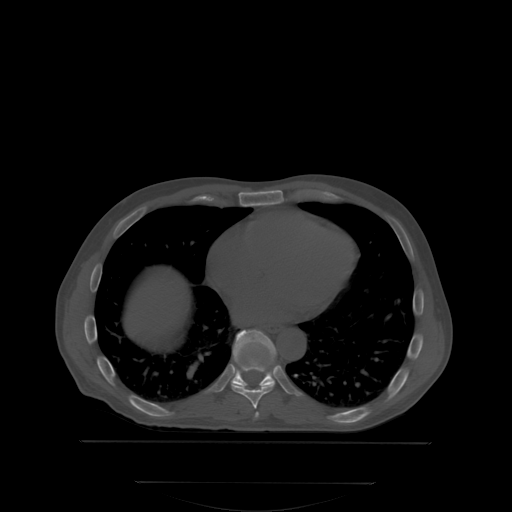
CT including the spine, one axial slice. Position 211 of 350 along the scan axis. Bone window (W 1800 / L 400 HU). 2.5 mm slice thickness. 512 × 512 image matrix, field of view 500 × 500 mm. Male patient, age 58 years. From the clinical record (not read from this slice): primary cancer: prostate.
Annotated regions visible in this slice (semi-automatically segmented with operator editing):
- T7 vertebra: bounding box (x1, y1, x2, y2) in pixels: (257, 413, 259, 415)
- T8 vertebra: (233, 354, 275, 409)
- T9 vertebra: (231, 330, 275, 388)